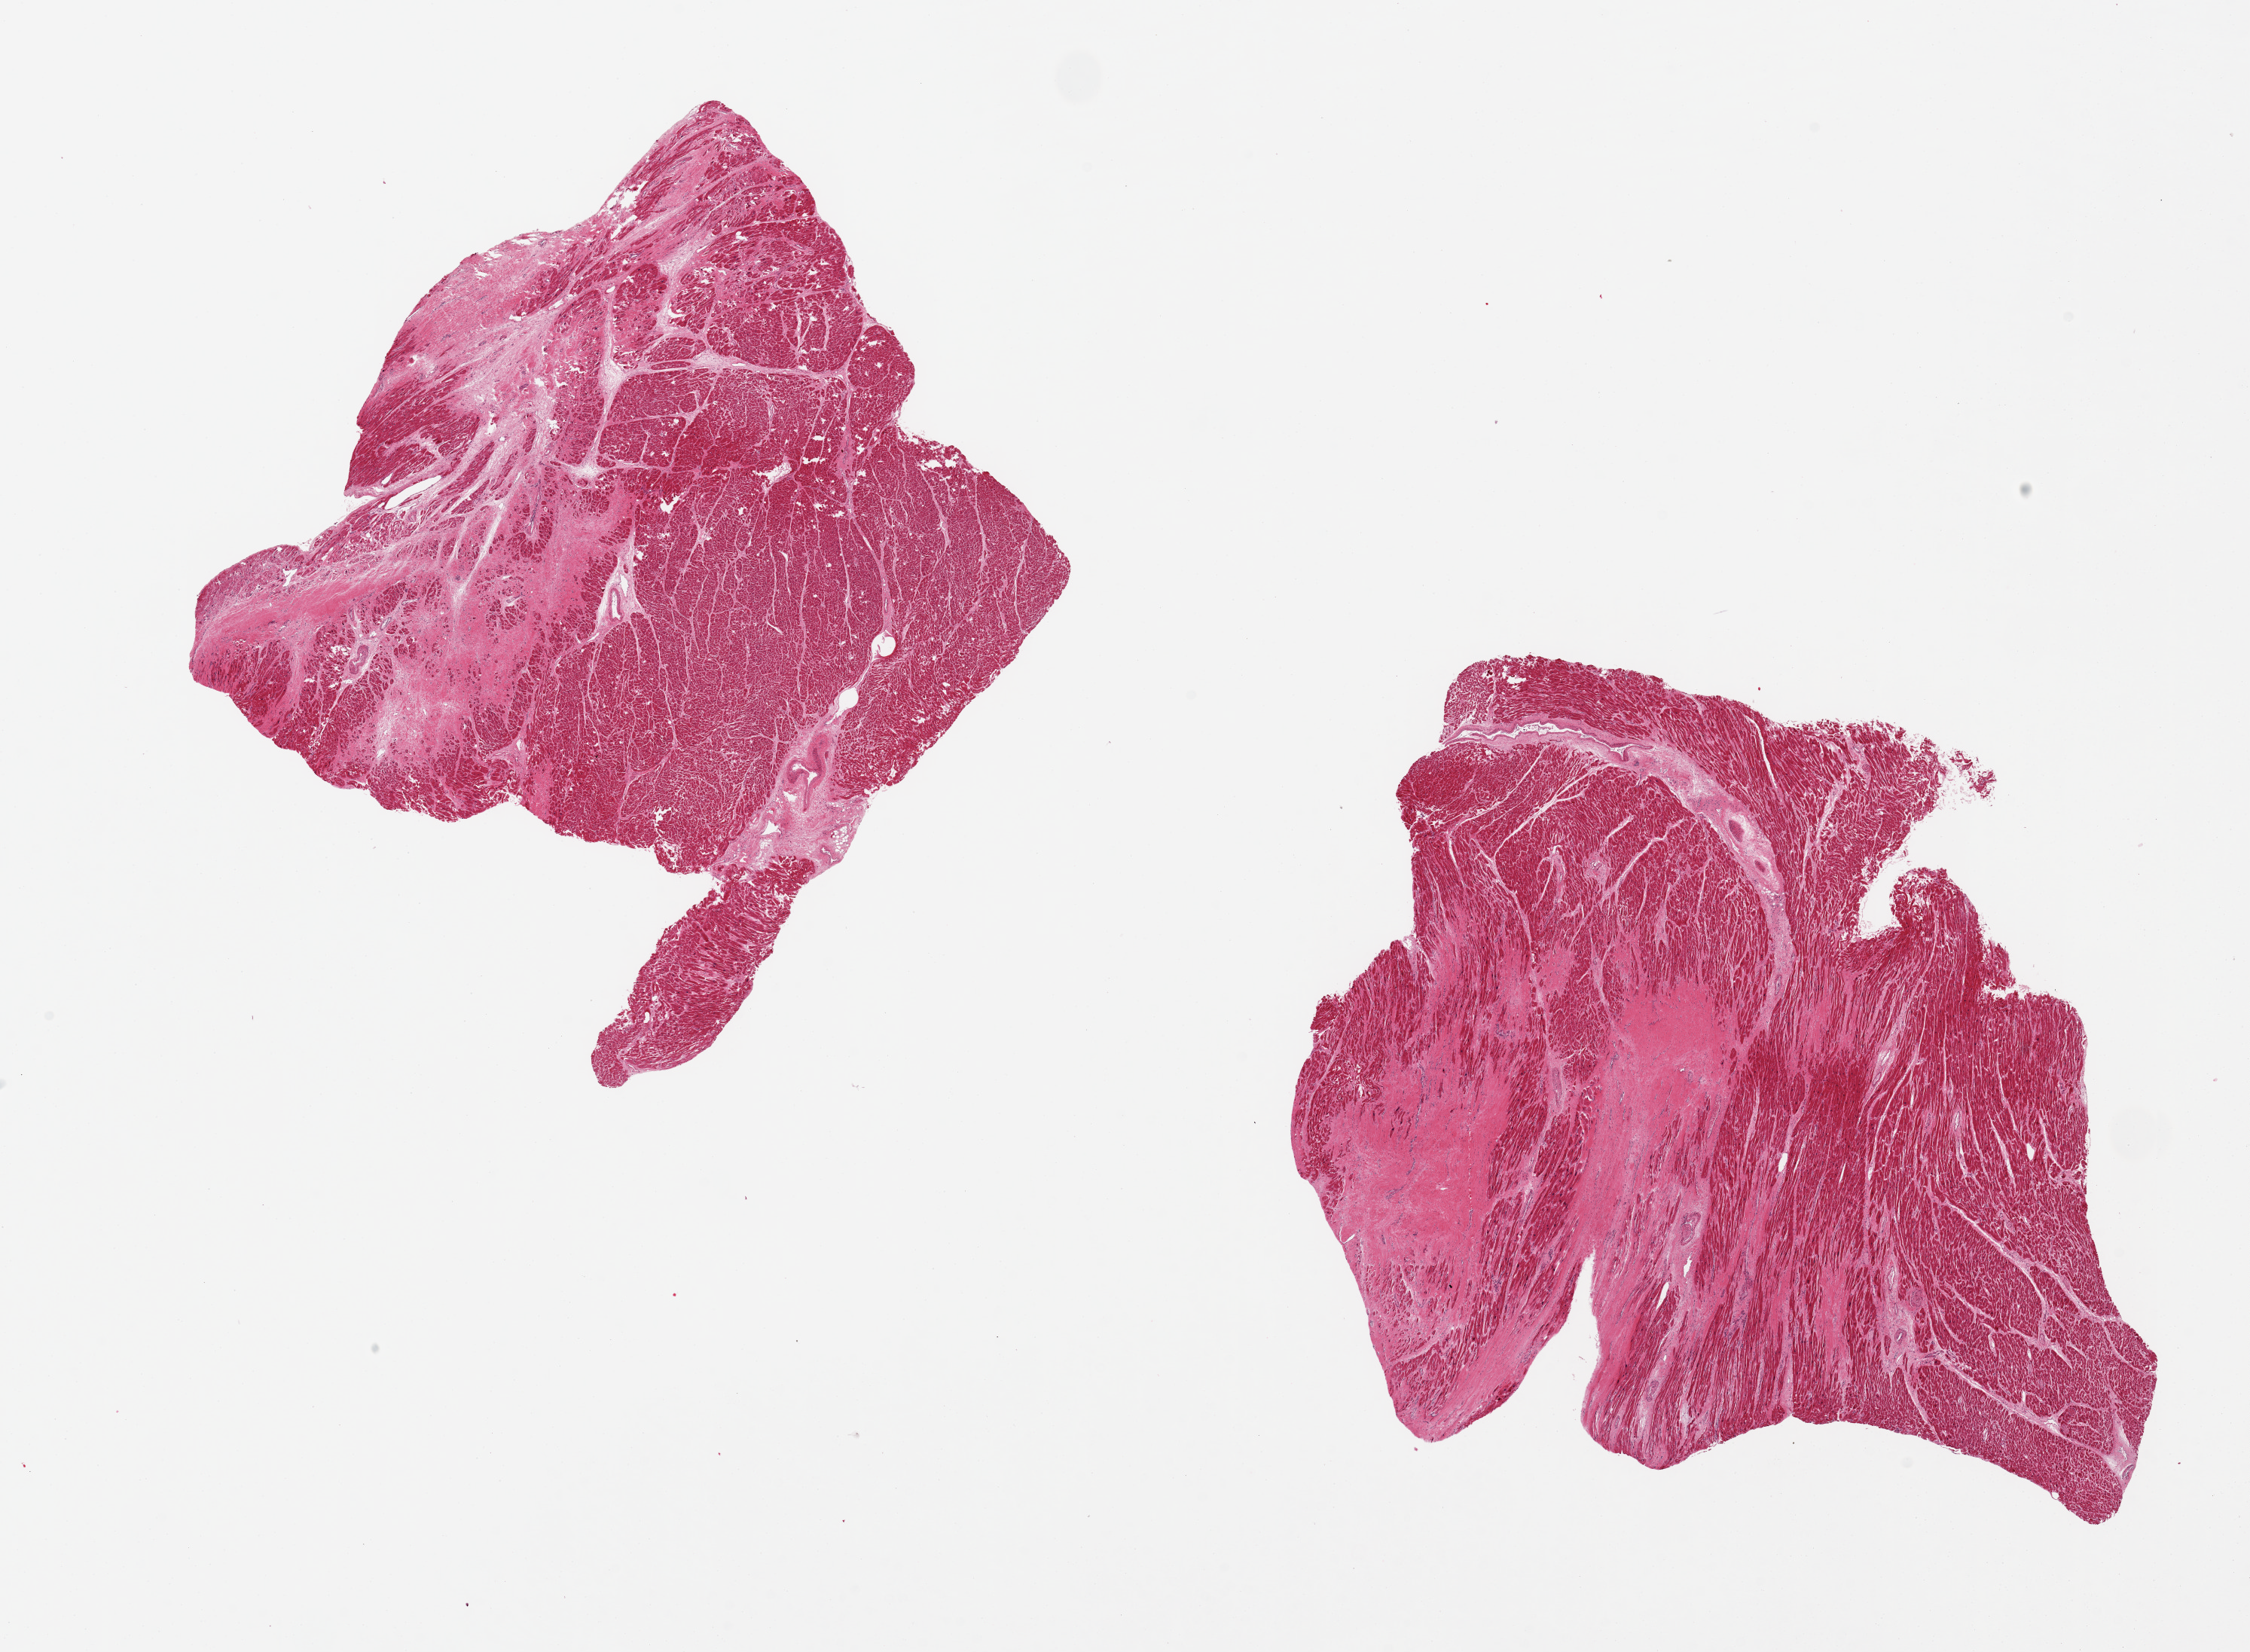
Whole-slide image, hematoxylin and eosin (H&E) stain, shown as a low-resolution overview of the whole scanned area (about 23.6 x 17.3 mm, acquisition: 20x scan). PAXgene-fixed paraffin-embedded (PFPE) section. Section of heart (target tissue). Tissue donor sample.
- reviewer comment on this tissue sample: 2 pieces; significant fibrosis consistent with history of infarction